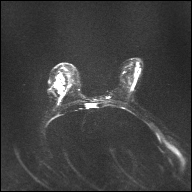
Breast MRI, one axial slice. Position 20 of 32 along the scan axis. Diffusion-weighted series; image 2 of 4 stored at this slice position (different b-values; order by instance number). 1.5 T. 4 mm slice thickness. 192 × 192 image matrix, field of view 360 × 360 mm. Female patient.
Outlined on this slice (outlined manually by an expert reader):
- tumour on diffusion-weighted imaging: box from (x=54, y=74) to (x=64, y=94) px